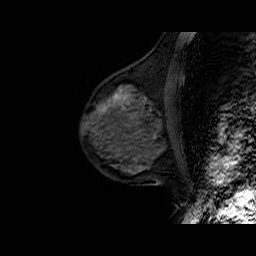
Breast MRI (dynamic contrast-enhanced), one sagittal slice; position 24 of 50 along the scan axis; dynamic contrast-enhanced series, time point 2 of 6 at this slice position (early post-contrast); 1.5 T; TE 6.5 ms, TR 32.9 ms; 4 mm slice thickness; 256 × 256 image matrix. Female patient. Case-level facts recorded for this patient, not image findings: setting: breast cancer imaged before/during neoadjuvant chemotherapy; receptor status: HR-positive, HER2-negative.
Outlined on this slice (semi-automatic segmentation, software-assisted and operator-edited):
- analysis volume of interest (the breast-tissue region the enhancement analysis was run in; not a lesion): box from (x=81, y=75) to (x=179, y=149) px
- tumour enhancement mask (voxels above the 100 % enhancement threshold inside the analysis volume of interest): (x=102, y=95)–(x=125, y=112)